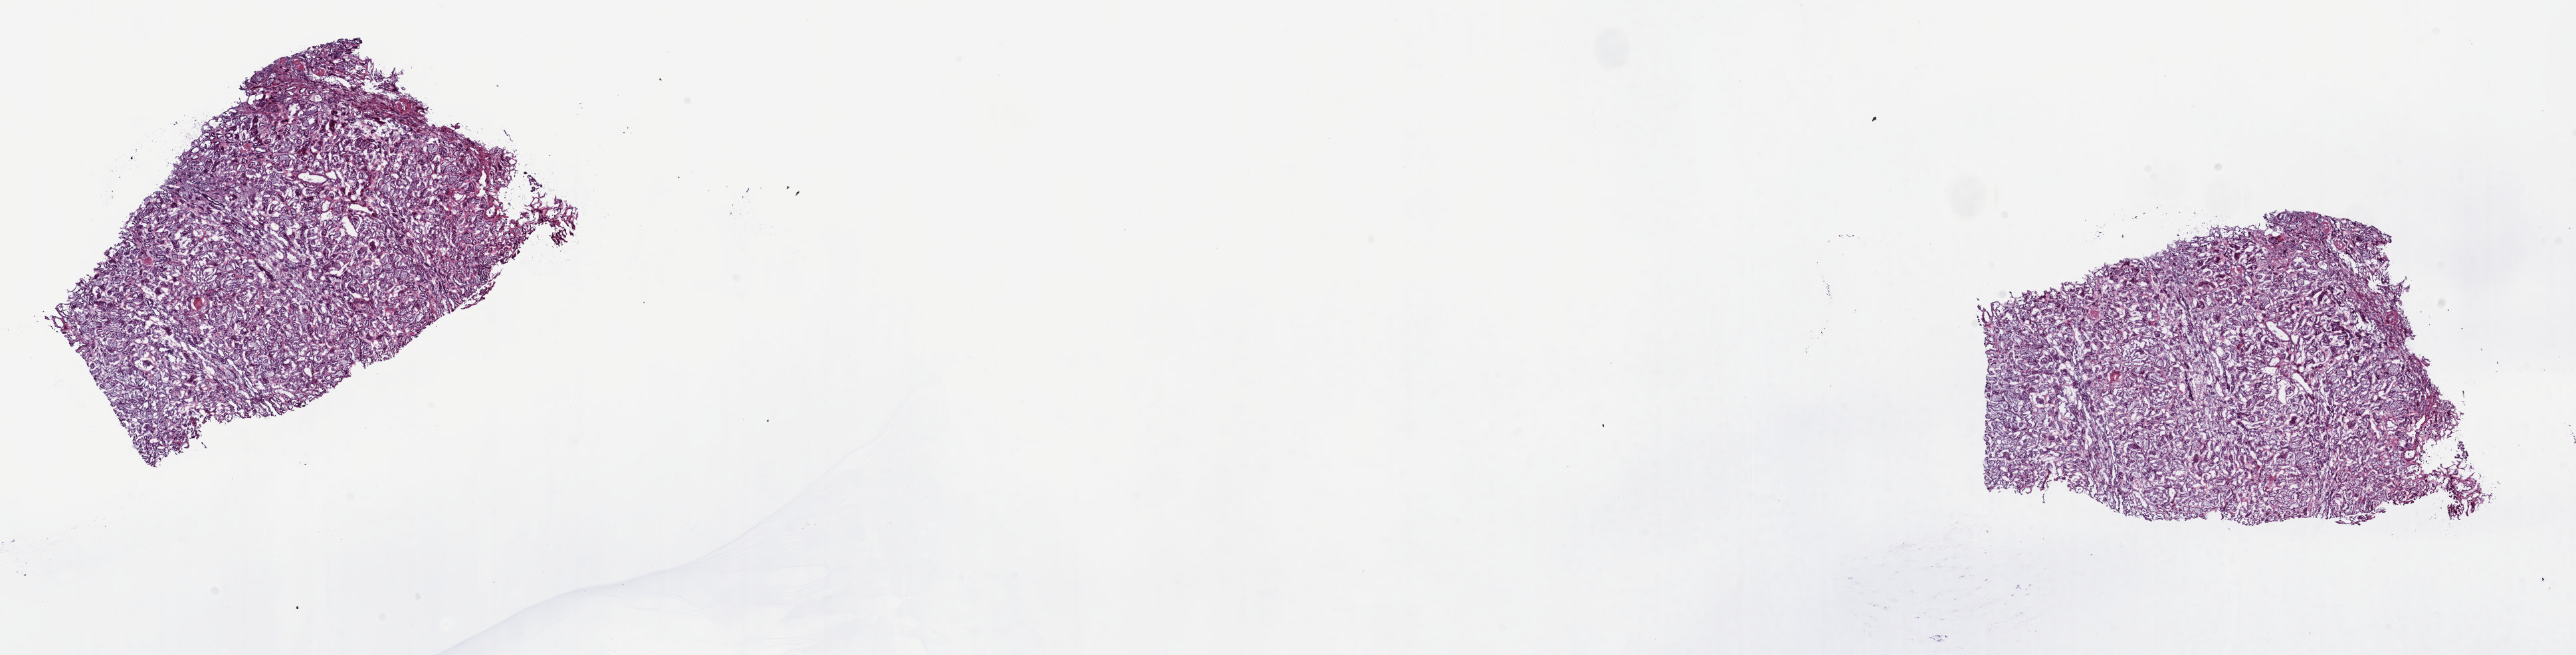
H&E-stained whole-slide image, a low-resolution overview of the entire scanned area, about 30.7 x 7.8 mm; frozen section from the top of the tissue portion; sample: solid tissue normal (non-tumour tissue), kidney. Male patient; age at initial diagnosis 69 years. Pathologist review of this section (percent, as recorded): tumour cells 0%, tumour nuclei 0%, normal cells 60%, stromal cells 40%, necrosis 0%. Infiltration values recorded for this section: lymphocyte infiltration 3%, monocyte infiltration 2%, neutrophil infiltration 2%.
• this section: solid tissue normal sample (biorepository sample class)
• patient diagnosis: Papillary adenocarcinoma, NOS